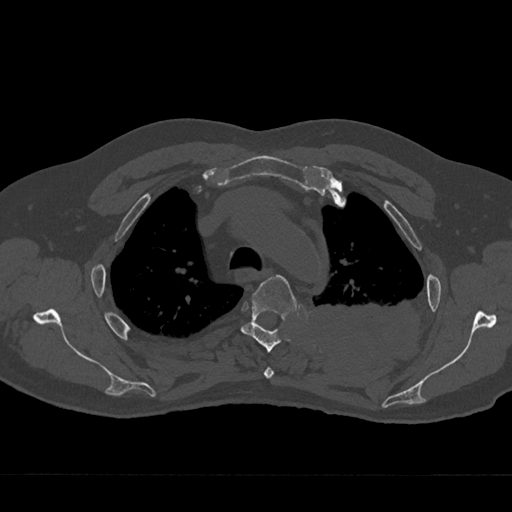
CT including the spine, one axial slice; 120 kVp; bone window (W 1800 / L 400 HU); 0.5 mm slice thickness; 512 × 512 image matrix, field of view 377 × 377 mm. Male patient, age 75 years. Case-level facts recorded for this patient, not image findings: primary cancer: renal; vertebrae with lytic lesions (as recorded): T4.
Structures marked on this image (semi-automatically segmented with operator editing):
- T3 vertebra: bounding box <264,367,274,379> (left, top, right, bottom; pixels)
- T4 vertebra: <241,275,296,352>